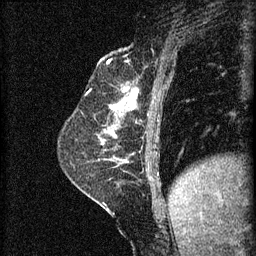
Breast MRI (dynamic contrast-enhanced), one sagittal slice; slice 21 of 60 in the series (ordered by position); 3 images stored at this slice position (order not interpretable as contrast timing); 1.5 T; TE 4.2 ms, TR 8.2 ms; 256 × 256 image matrix, field of view 180 × 180 mm. Female patient, age 59 years.
Outlined on this slice (semi-automatic segmentation, software-assisted and operator-edited):
- analysis volume of interest (the breast-tissue region the enhancement analysis was run in; not a lesion): box from (x=98, y=92) to (x=137, y=135) px
- tumour enhancement mask (voxels above the 70 % enhancement threshold inside the analysis volume of interest): (x=112, y=92)–(x=137, y=111)